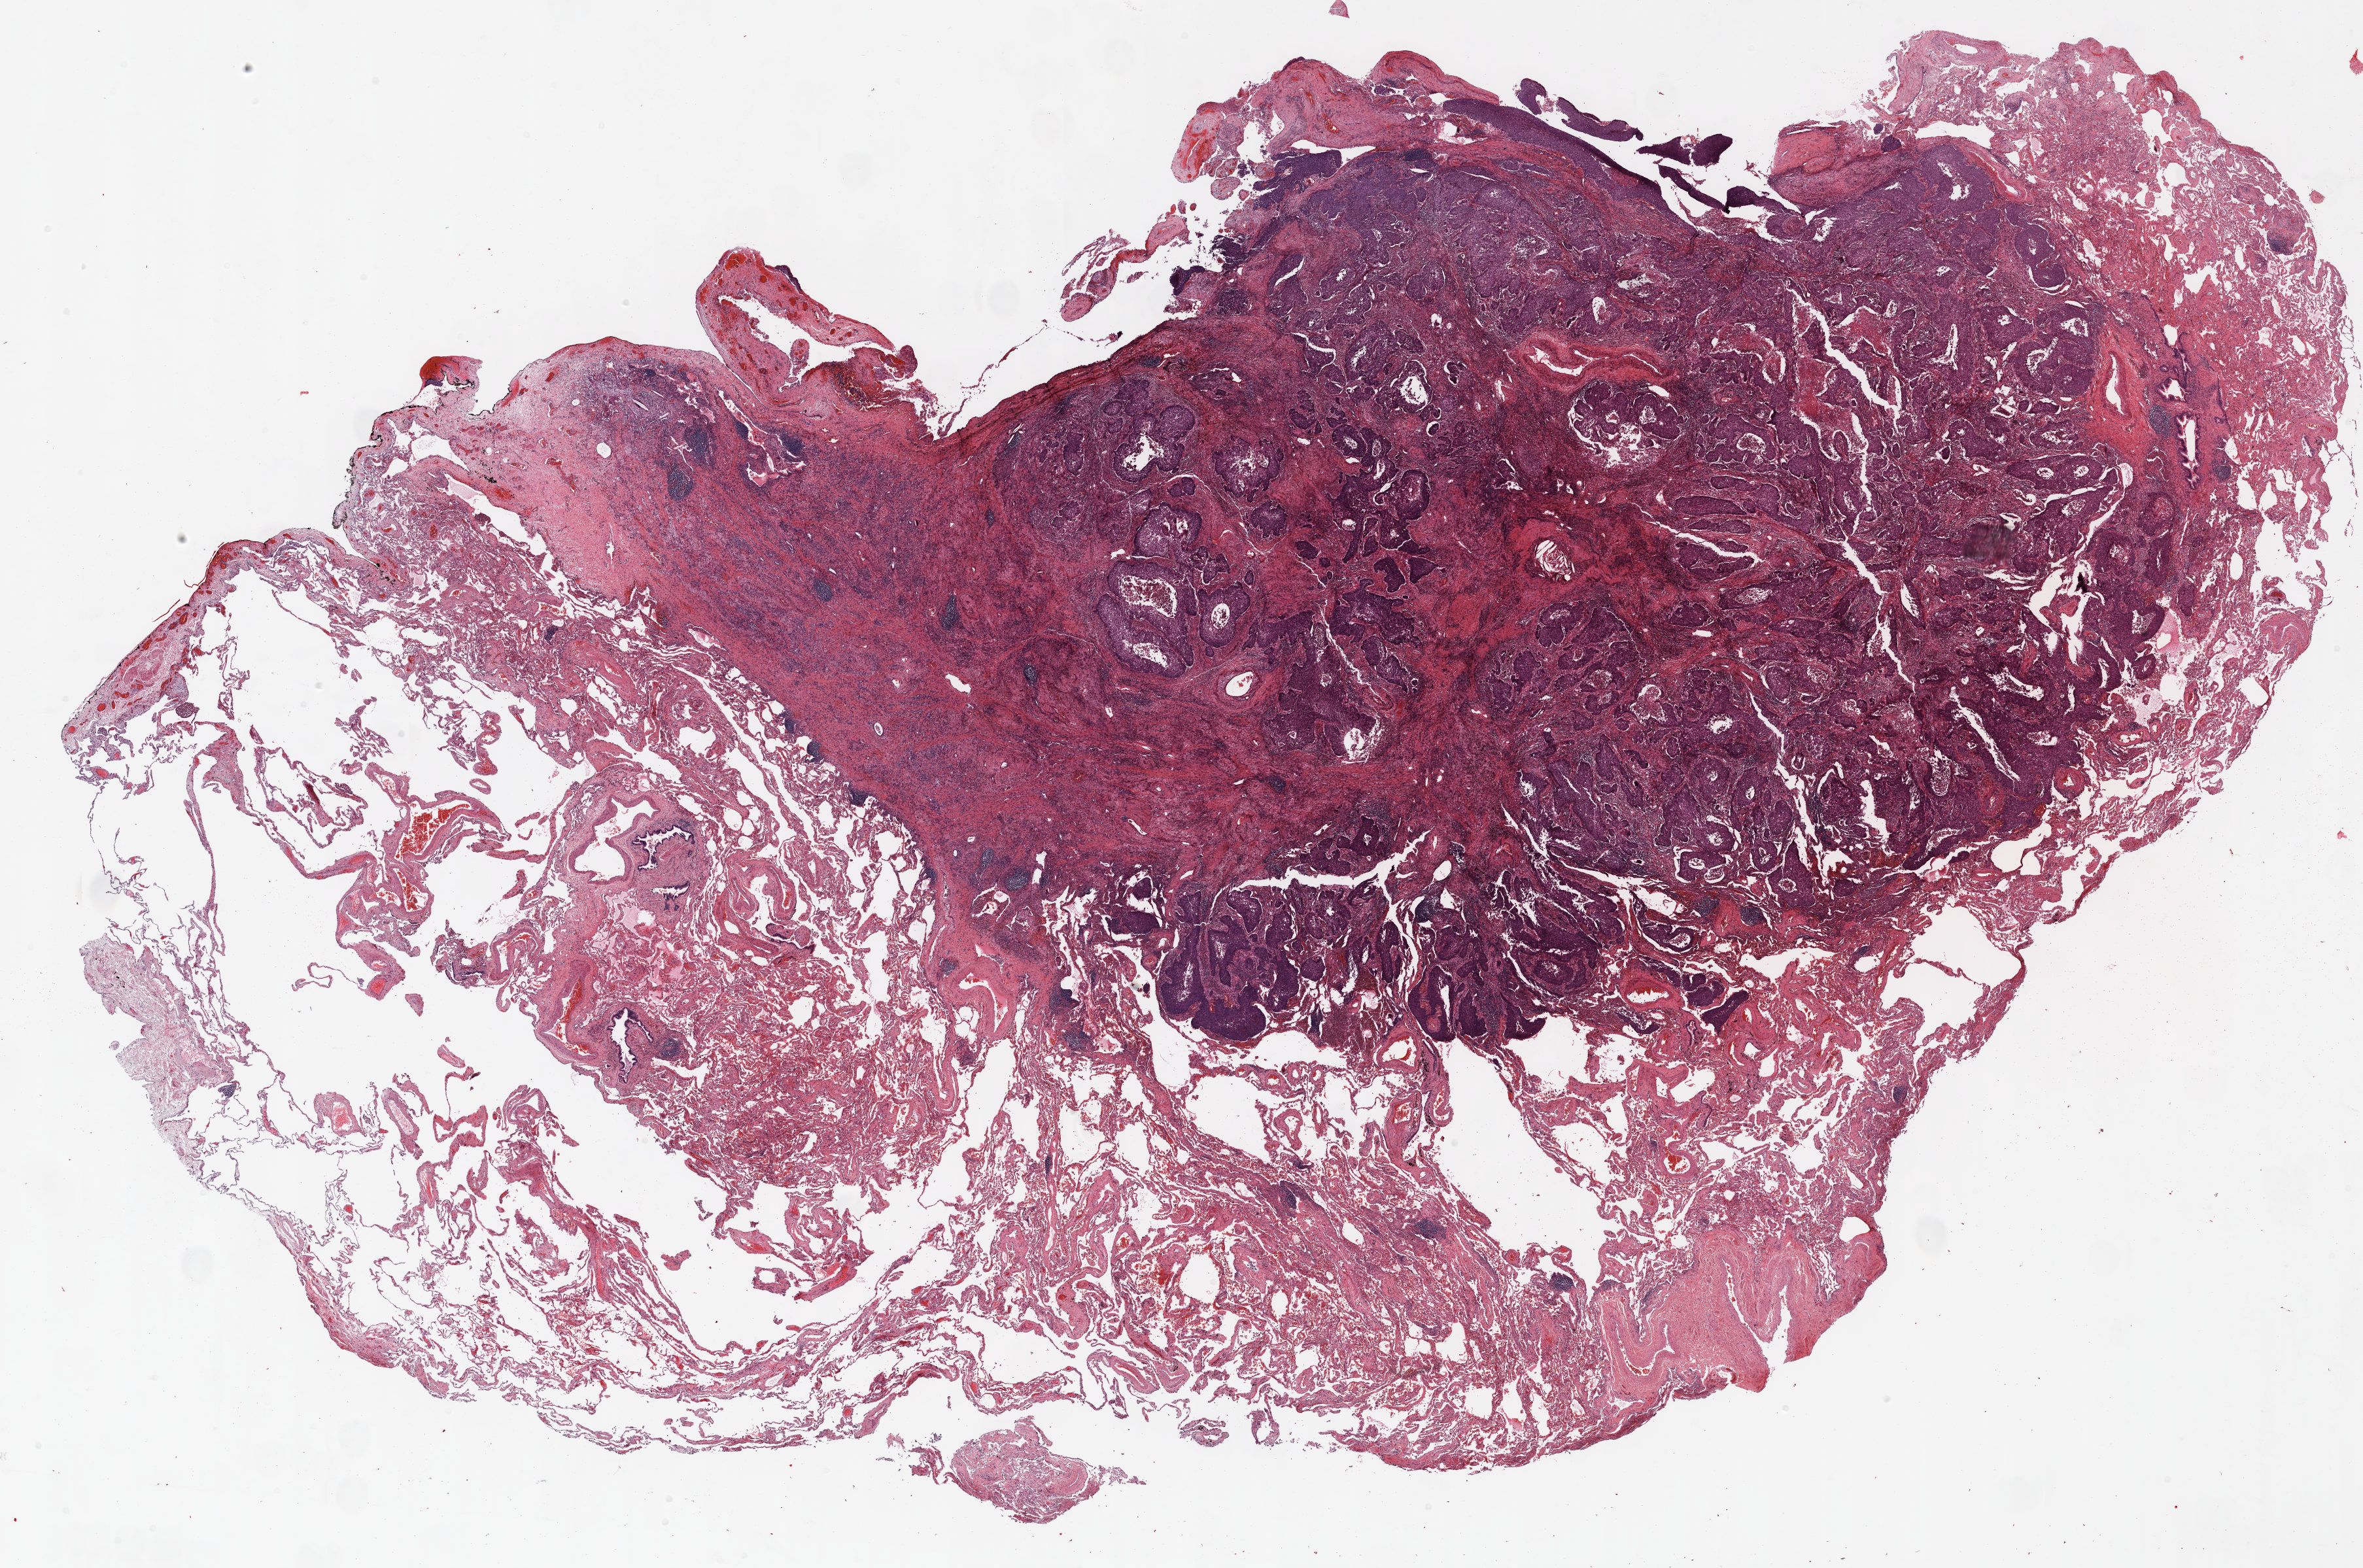
H&E-stained whole-slide image — whole scanned area (about 29.0 x 19.3 mm) shown as a low-resolution overview. FFPE section. Lung tissue. Male, age 66 at enrolment. Current smoker at enrolment.
Participant's lung-cancer diagnosis: Squamous cell carcinoma, NOS (ICD-O-3 8070/3). Note: participant had 2 primary lung cancers recorded; fields above describe the first.